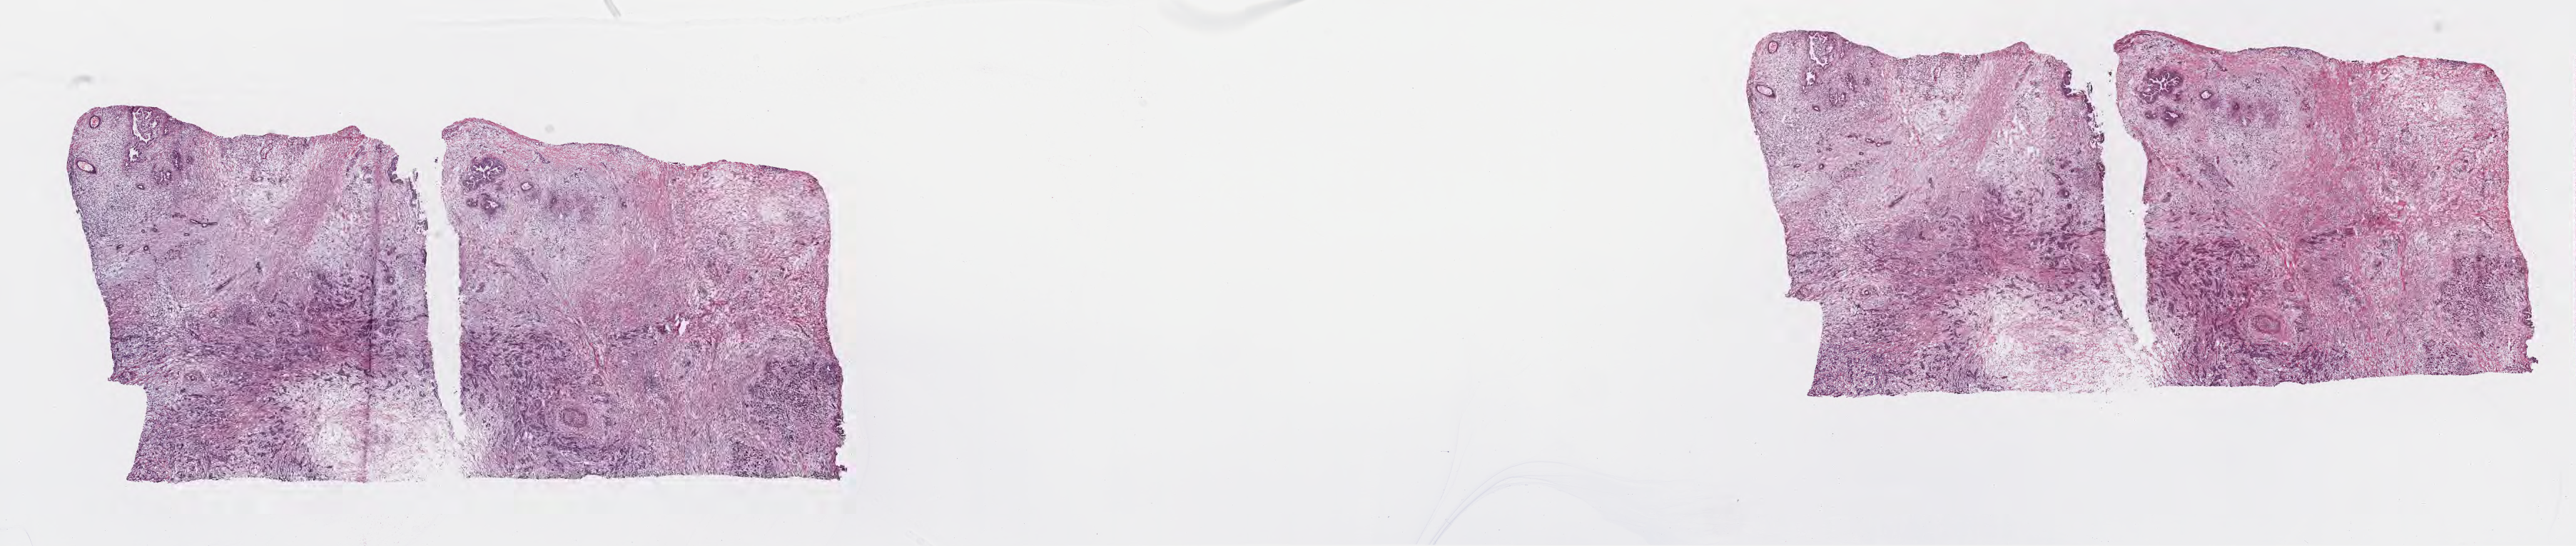
Hematoxylin and eosin (H&E) whole-slide image — a low-resolution overview of the entire scanned area, about 29.2 x 6.2 mm; frozen section (tissue freezing medium); specimen: primary tumor; site: head of pancreas. Female, age 64 years at initial diagnosis. Composition of this section per pathologist review: tumor cells 22%, tumor nuclei 65%, stromal cells 67%, necrosis 11%, normal cells 0%. Infiltration values recorded for this section: lymphocyte infiltration 22%, monocyte infiltration 1%, neutrophil infiltration 0%.
* section: top of the tissue portion
* histologic diagnosis: Infiltrating duct carcinoma, NOS